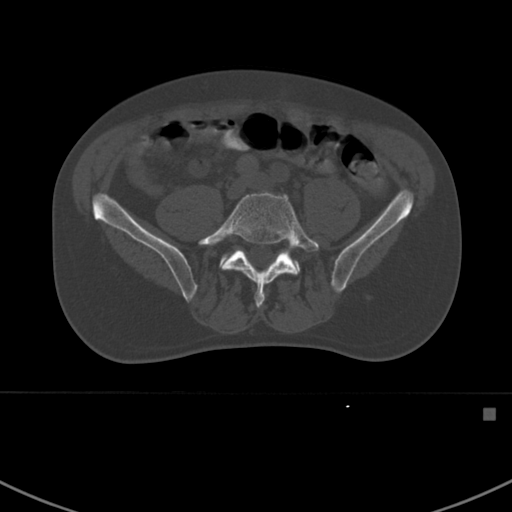
CT including the spine, one axial slice; position 218 of 412 along the scan axis; reconstruction kernel Br40s; 120 kVp; bone window (W 1800 / L 400 HU); 512 × 512 image matrix. Male patient, age 59 years. Case-level facts recorded for this patient, not image findings: primary cancer: prostate.
Outlined on this slice (semi-automatically segmented with operator editing):
- L5 vertebra: box from (x=198, y=190) to (x=319, y=309) px